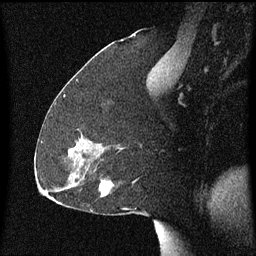
Breast MRI (dynamic contrast-enhanced), one sagittal slice. Slice 32 of 60 in the series (ordered by position). Dynamic contrast-enhanced series, image 2 of 3 at this slice position (ordered by acquisition). 1.5 T. TE 4.2 ms, TR 8.4 ms. 2 mm slice thickness. 256 × 256 image matrix, field of view 200 × 200 mm. Female patient, age 59 years.
Annotated regions visible in this slice (semi-automatic segmentation, software-assisted and operator-edited):
- analysis volume of interest (the breast-tissue region the enhancement analysis was run in; not a lesion): bounding box (x1, y1, x2, y2) in pixels: (94, 170, 137, 197)
- tumour enhancement mask (voxels above the 70 % enhancement threshold inside the analysis volume of interest): (100, 182, 109, 195)